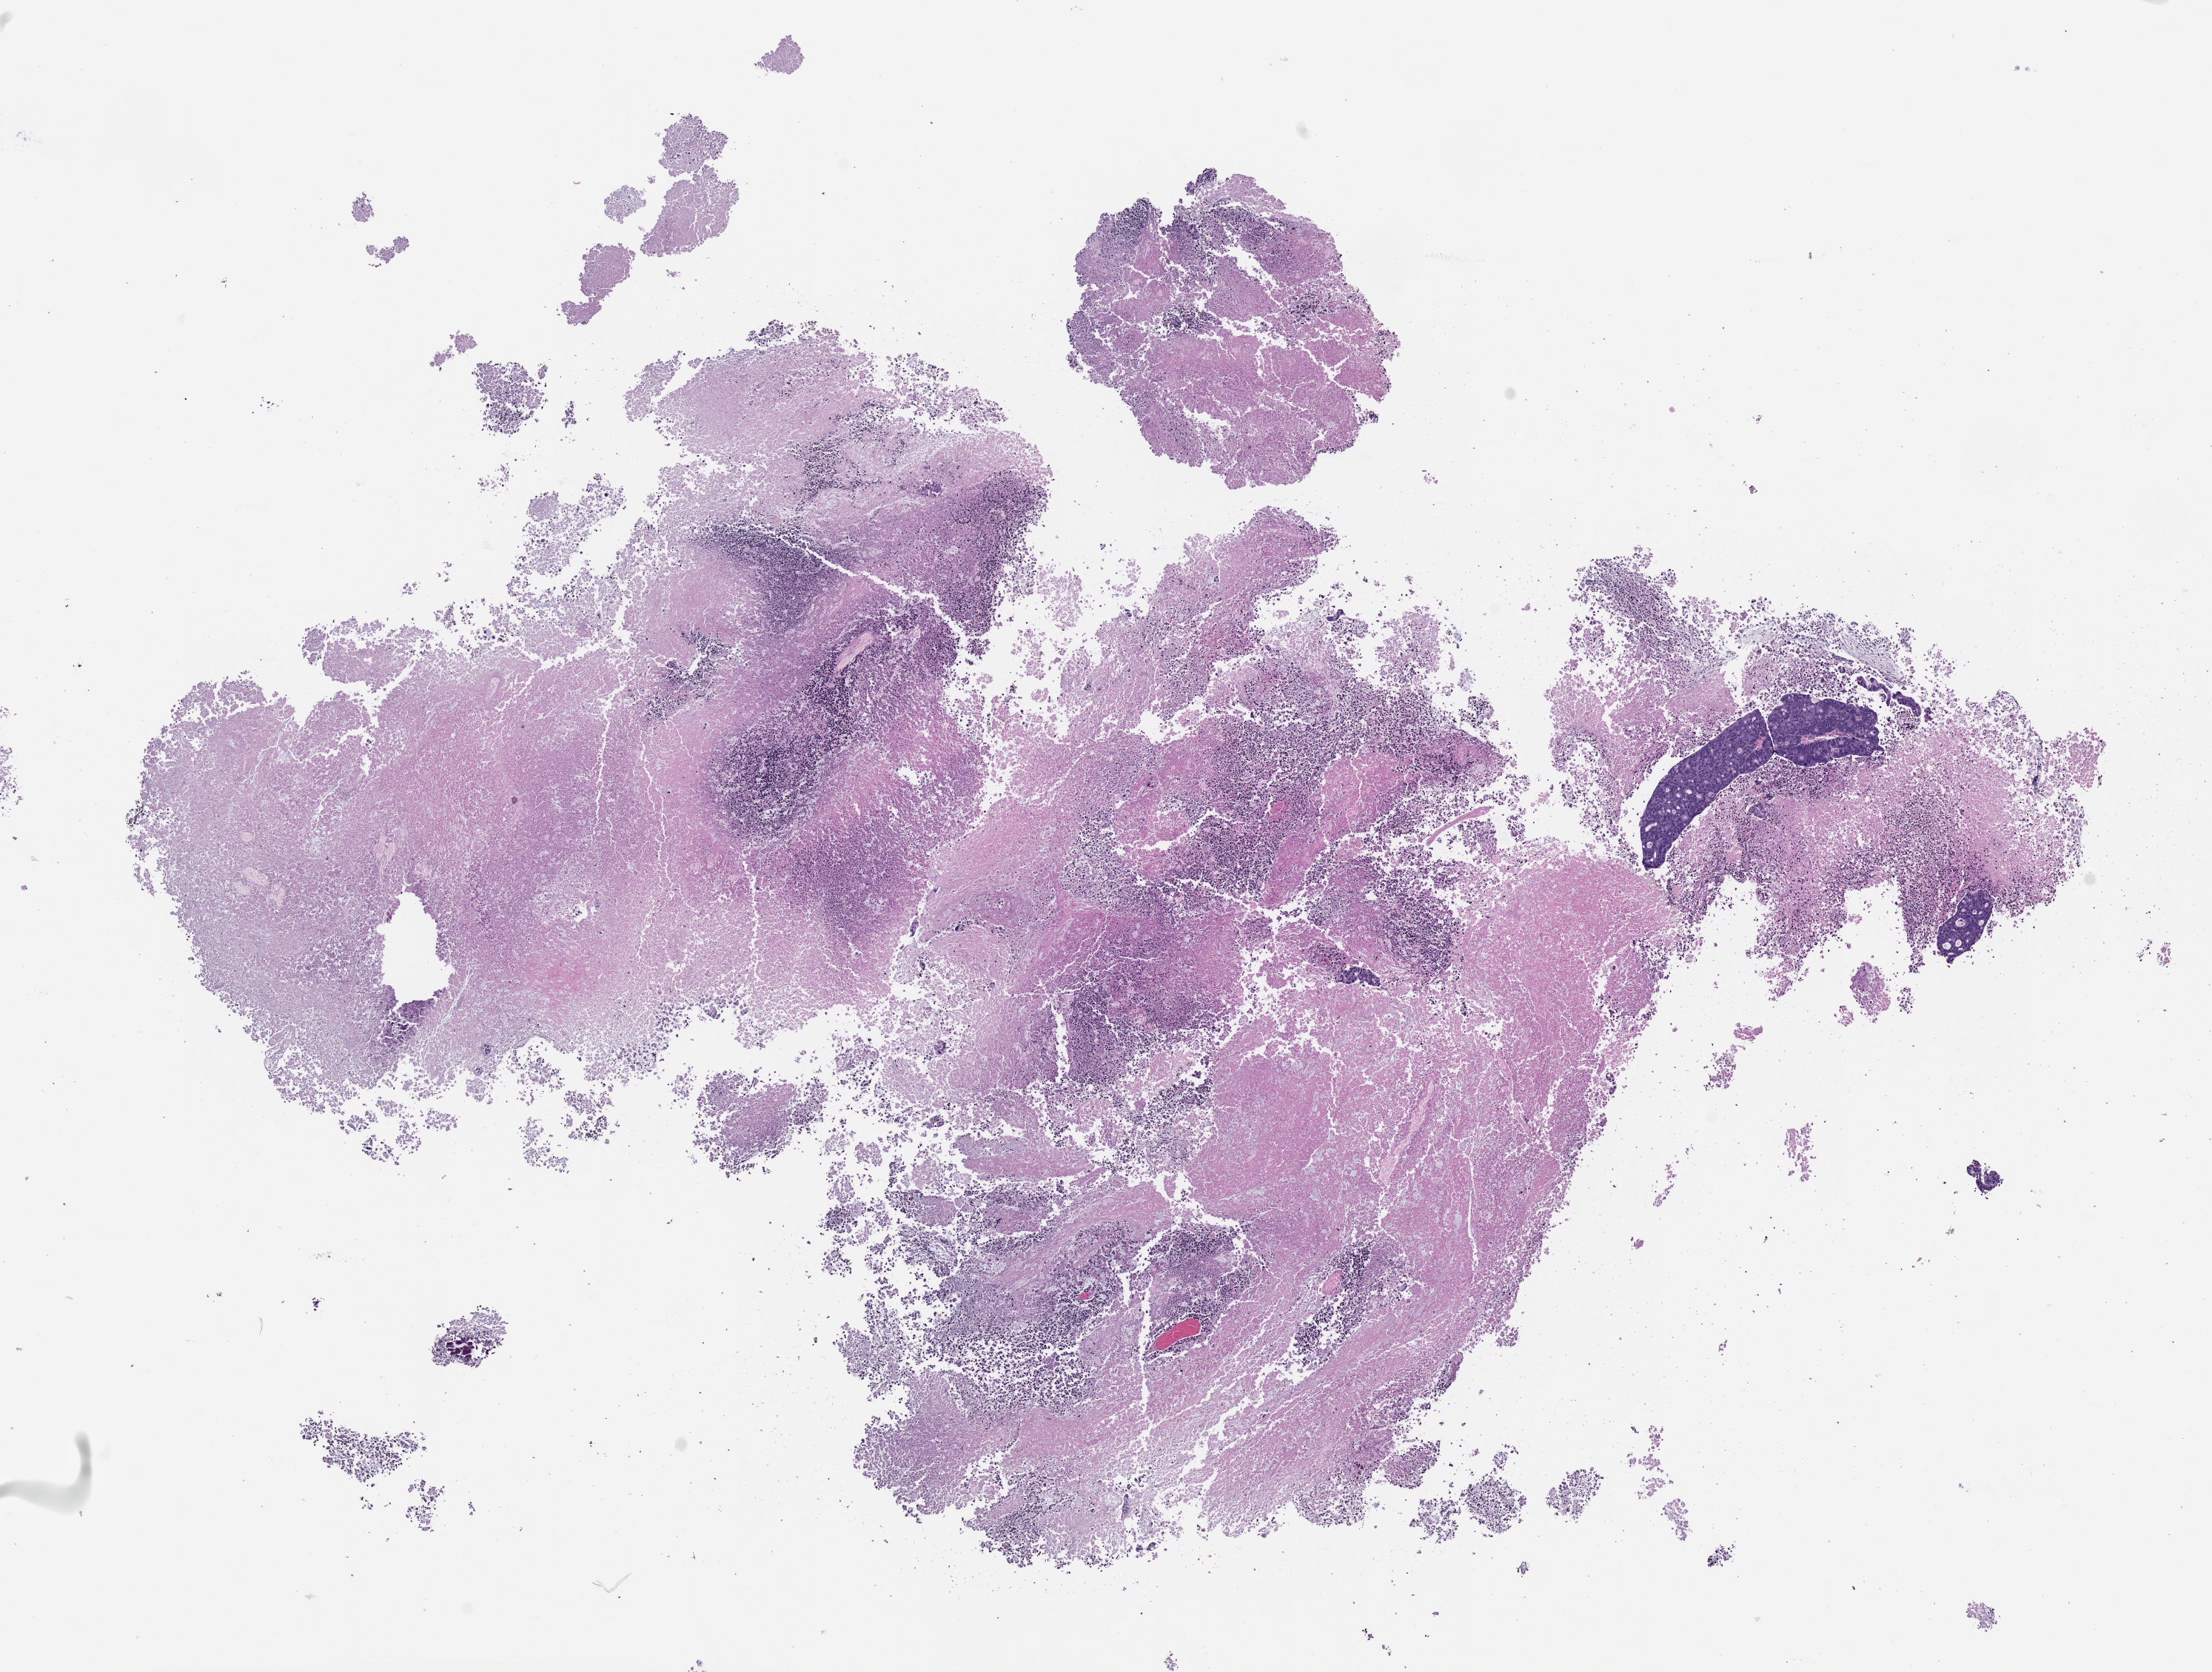
Whole-slide image, haematoxylin and eosin: patient-derived xenograft (human tumor grown in a mouse), passage 2, whole scanned area (about 12.0 x 9.1 mm) shown as a low-resolution overview. Formalin-fixed, paraffin-embedded (FFPE) tissue. Originating tumor site category: gastrointestinal tract.
Originating patient diagnosis: Colorectal Carcinoma.